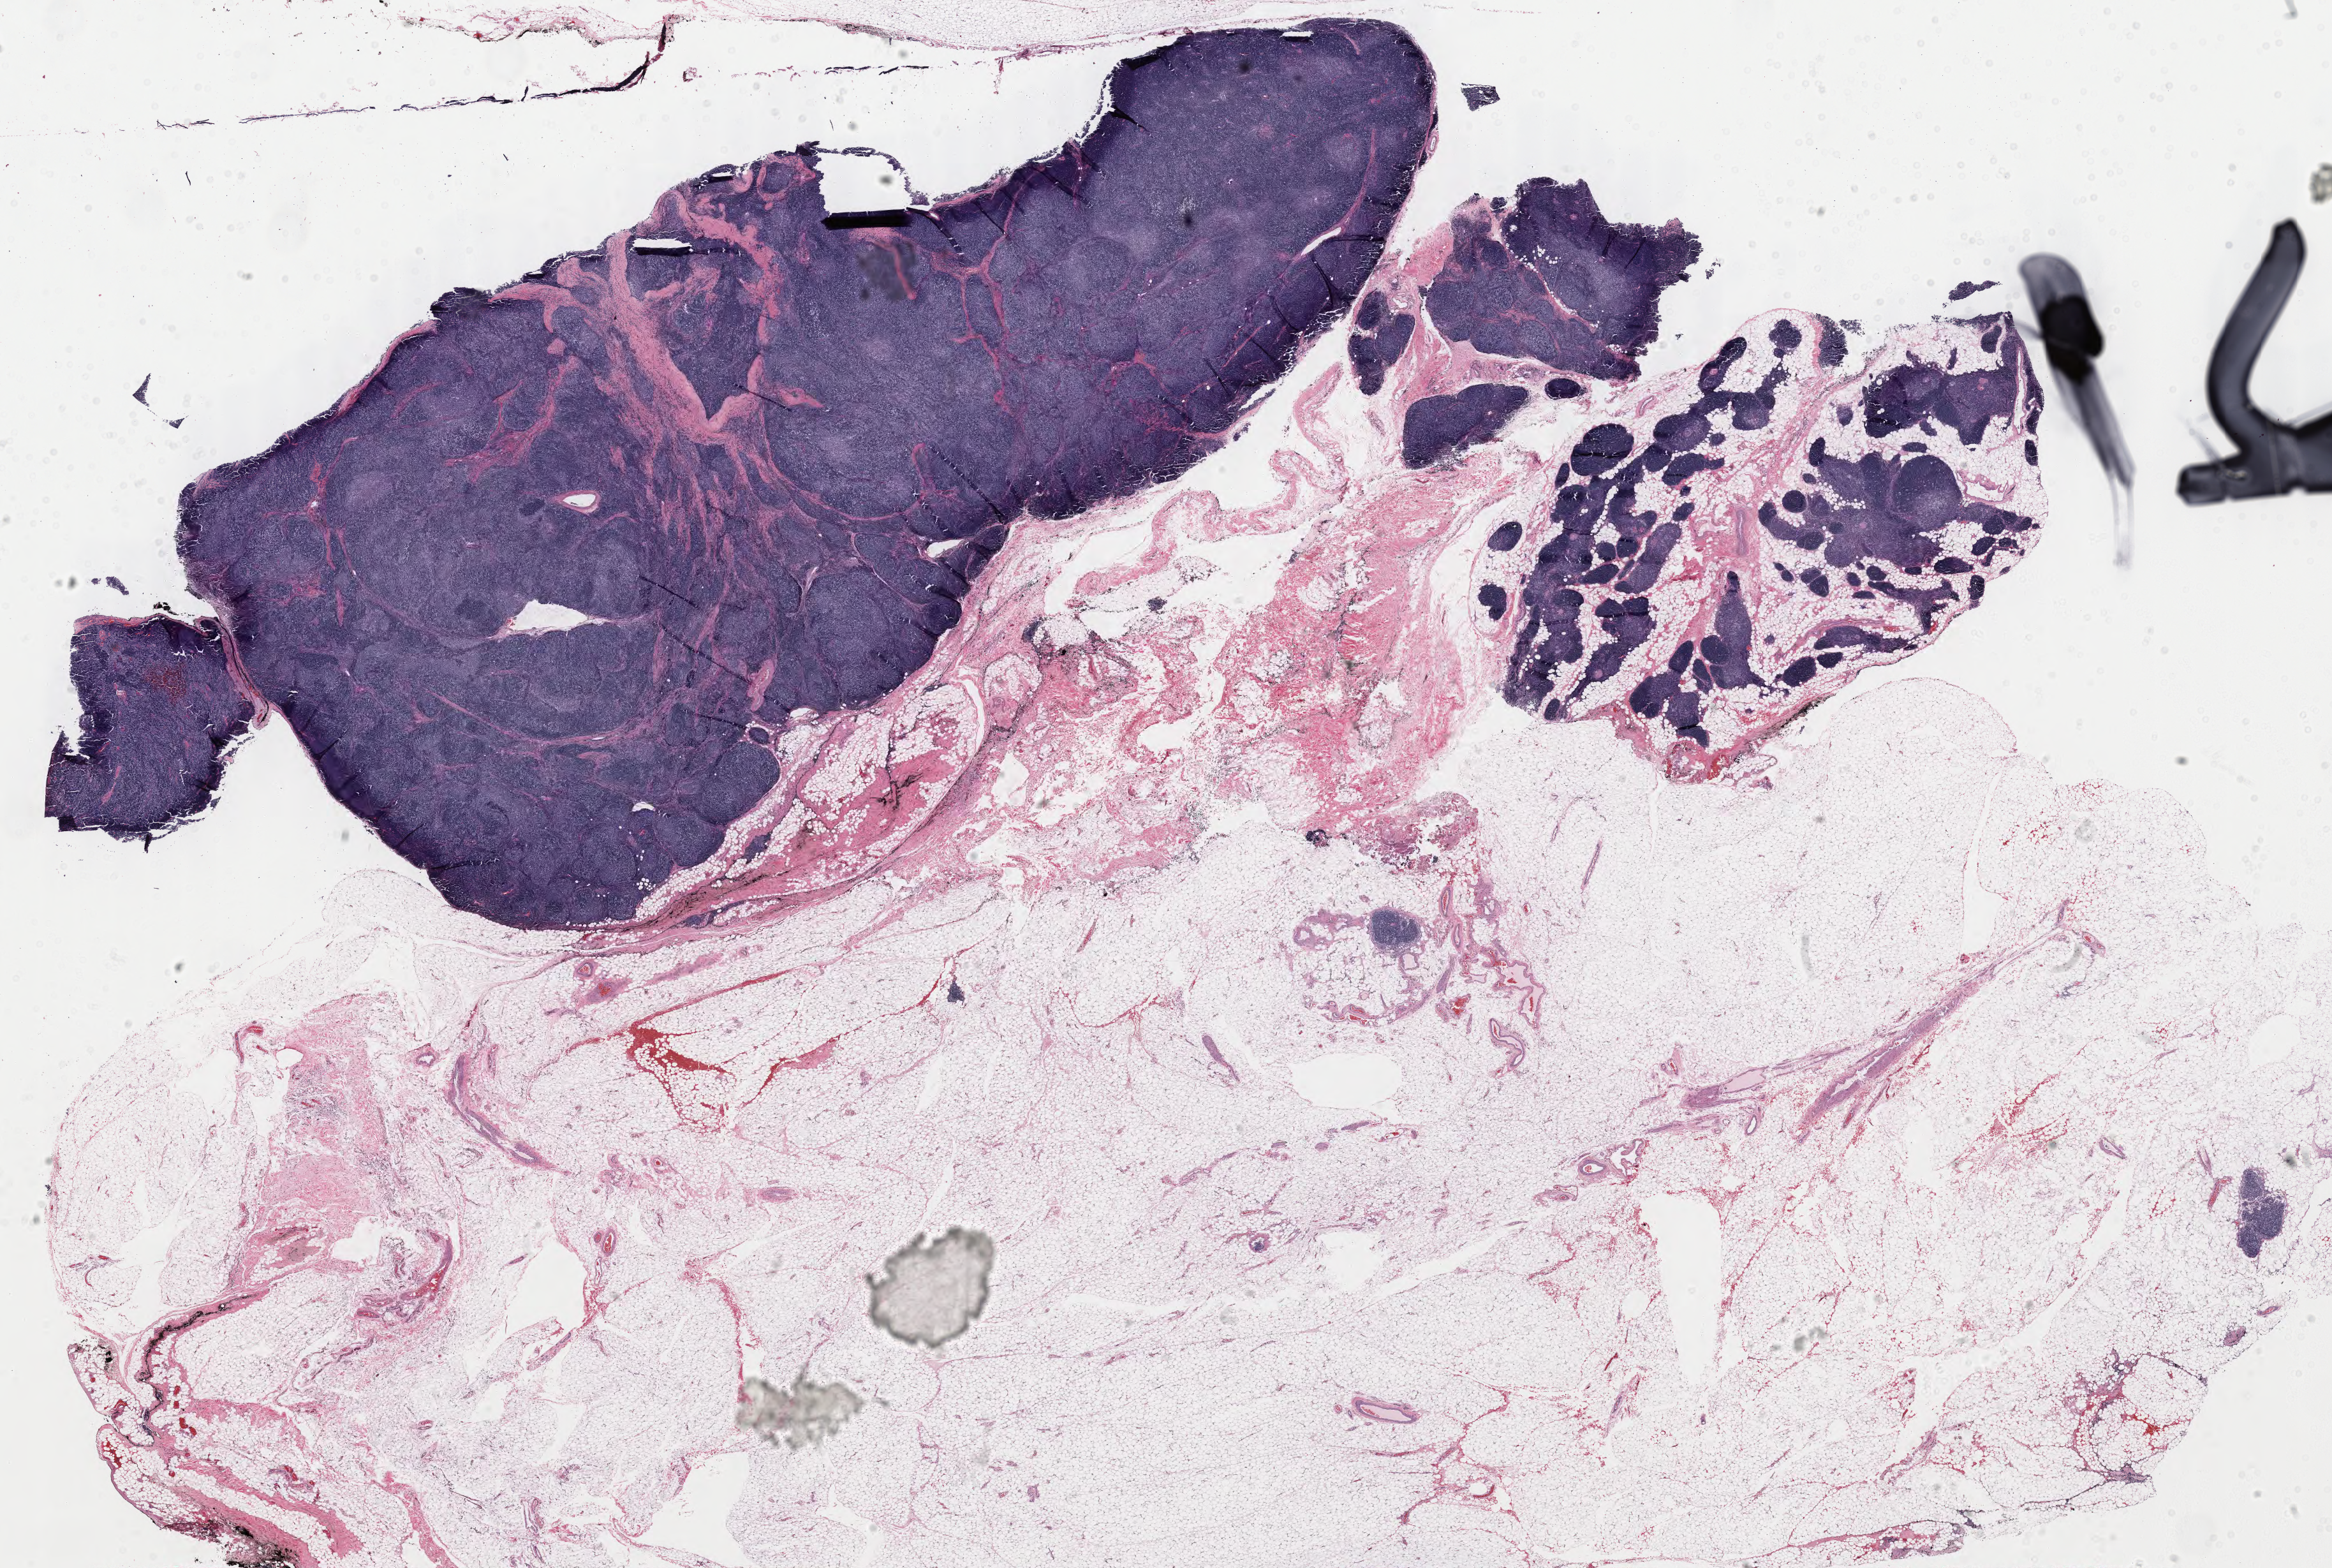
H&E whole-slide image — whole scanned area (about 29.0 x 19.5 mm) shown as a low-resolution overview. Formalin-fixed paraffin-embedded (FFPE) diagnostic section. Thymus, primary tumour sample. Male patient; age at initial diagnosis 44 years.
* diagnosis: Thymoma, type B2, malignant